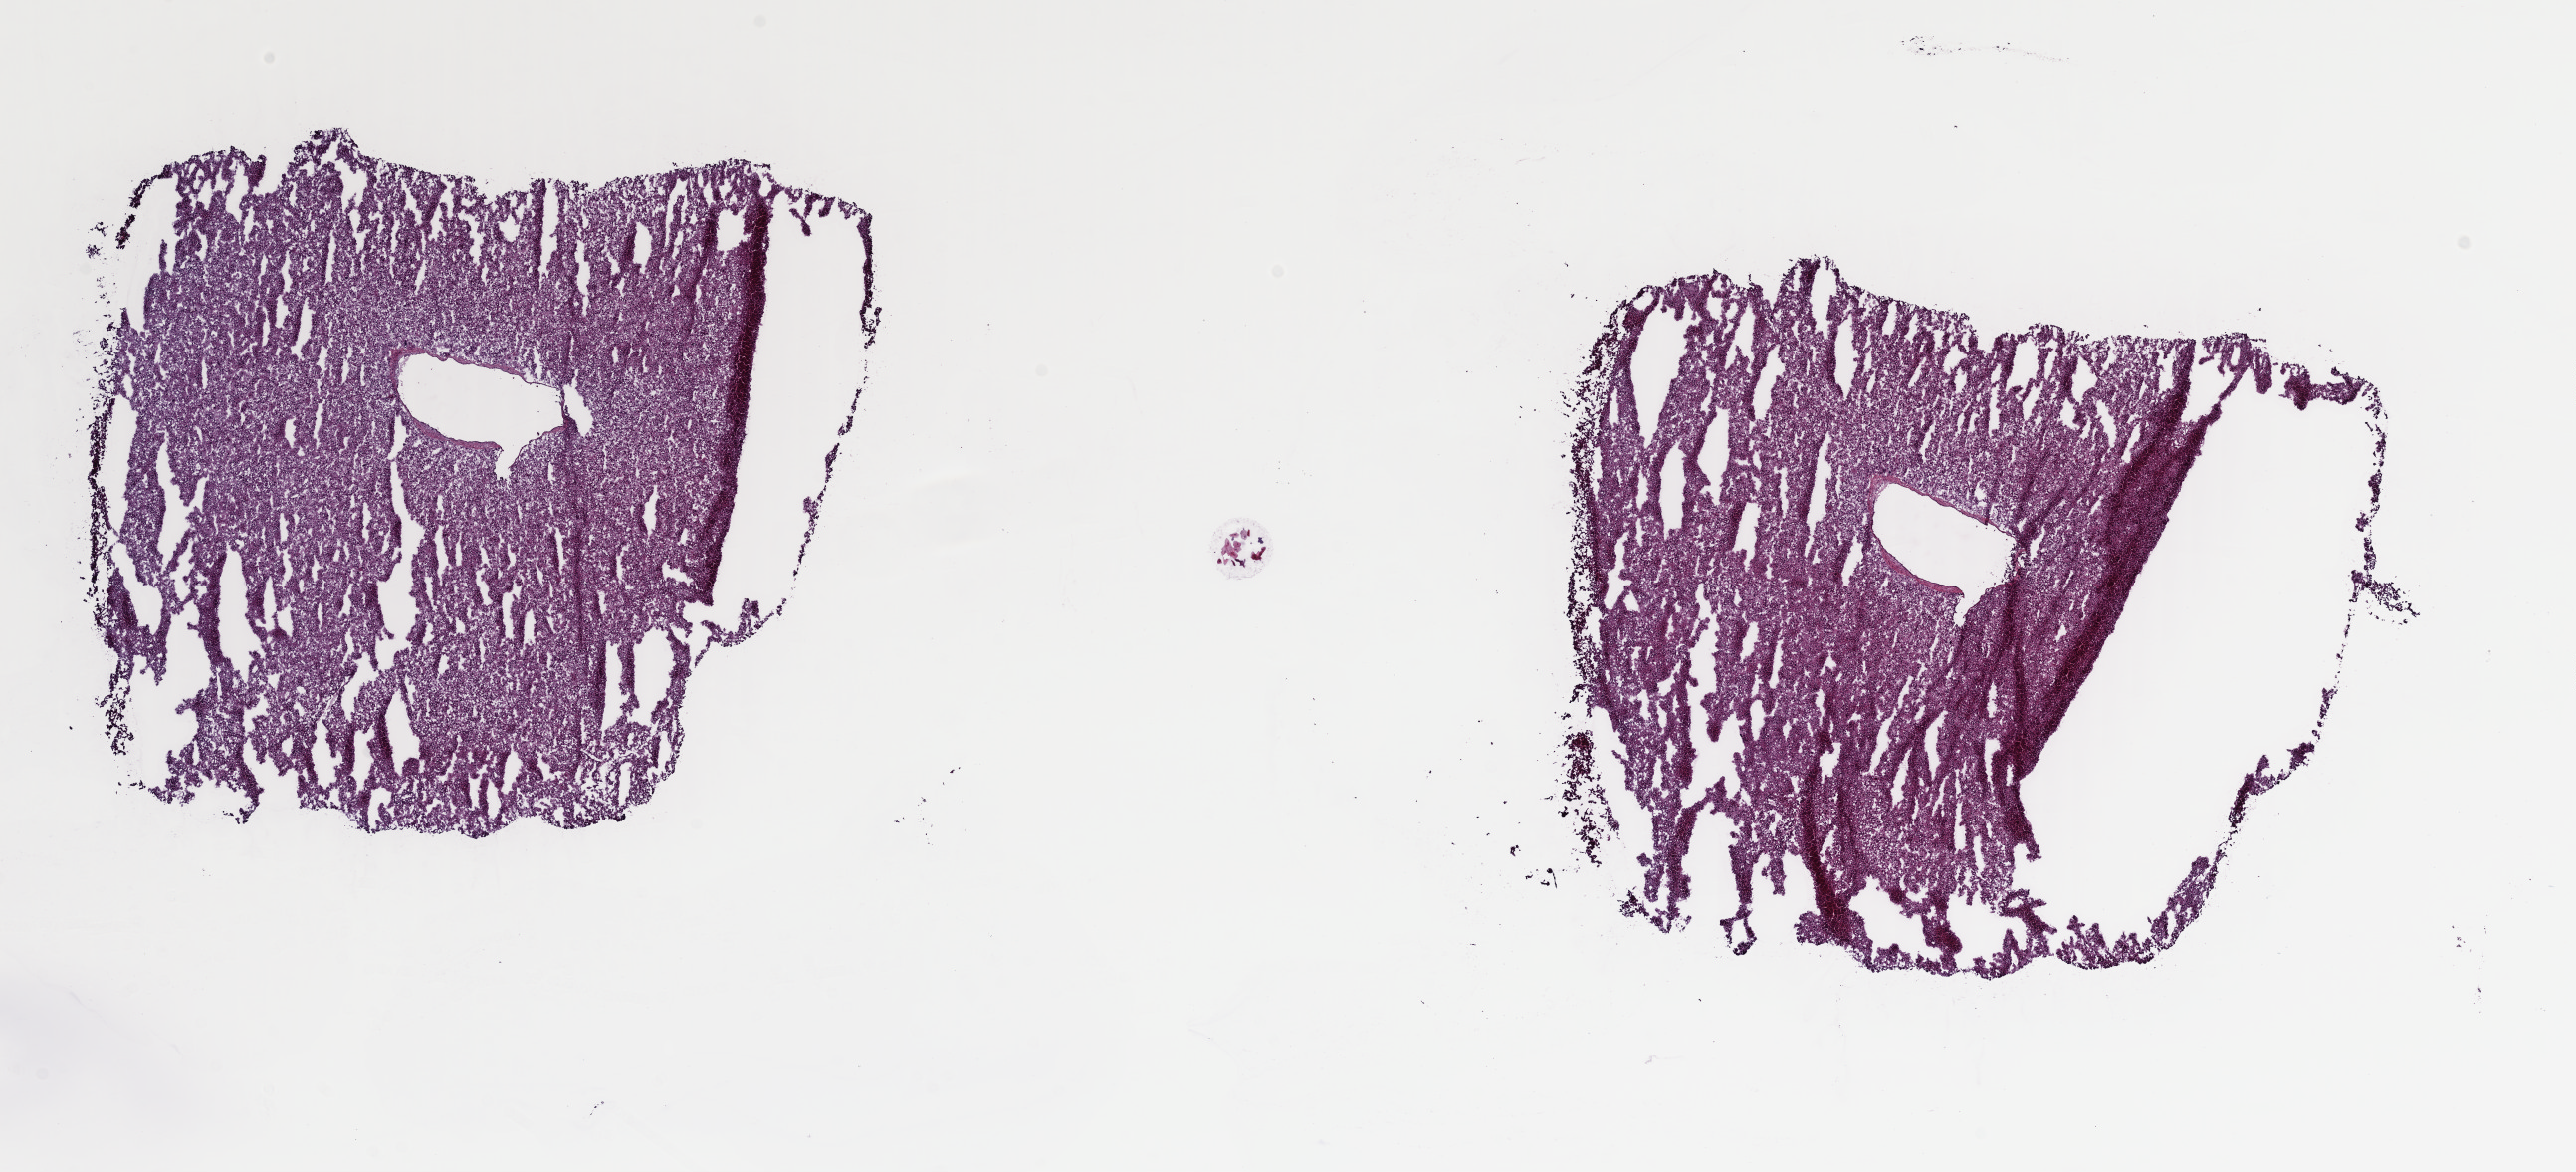
Hematoxylin and eosin (H&E) stained whole-slide image, low-resolution overview of the scanned area, about 20.4 x 9.3 mm. Frozen section from the top of the tissue portion. Primary tumour sample from the adrenal cortex. Female patient; age at initial diagnosis 64 years. Composition of this section per pathologist review: tumour cells 100%, tumour nuclei 97%, normal cells 0%, stromal cells 0%, necrosis 0%. Infiltration values recorded for this section: lymphocyte infiltration 0%, monocyte infiltration 0%, neutrophil infiltration 0%.
* histologic diagnosis: Adrenal cortical carcinoma